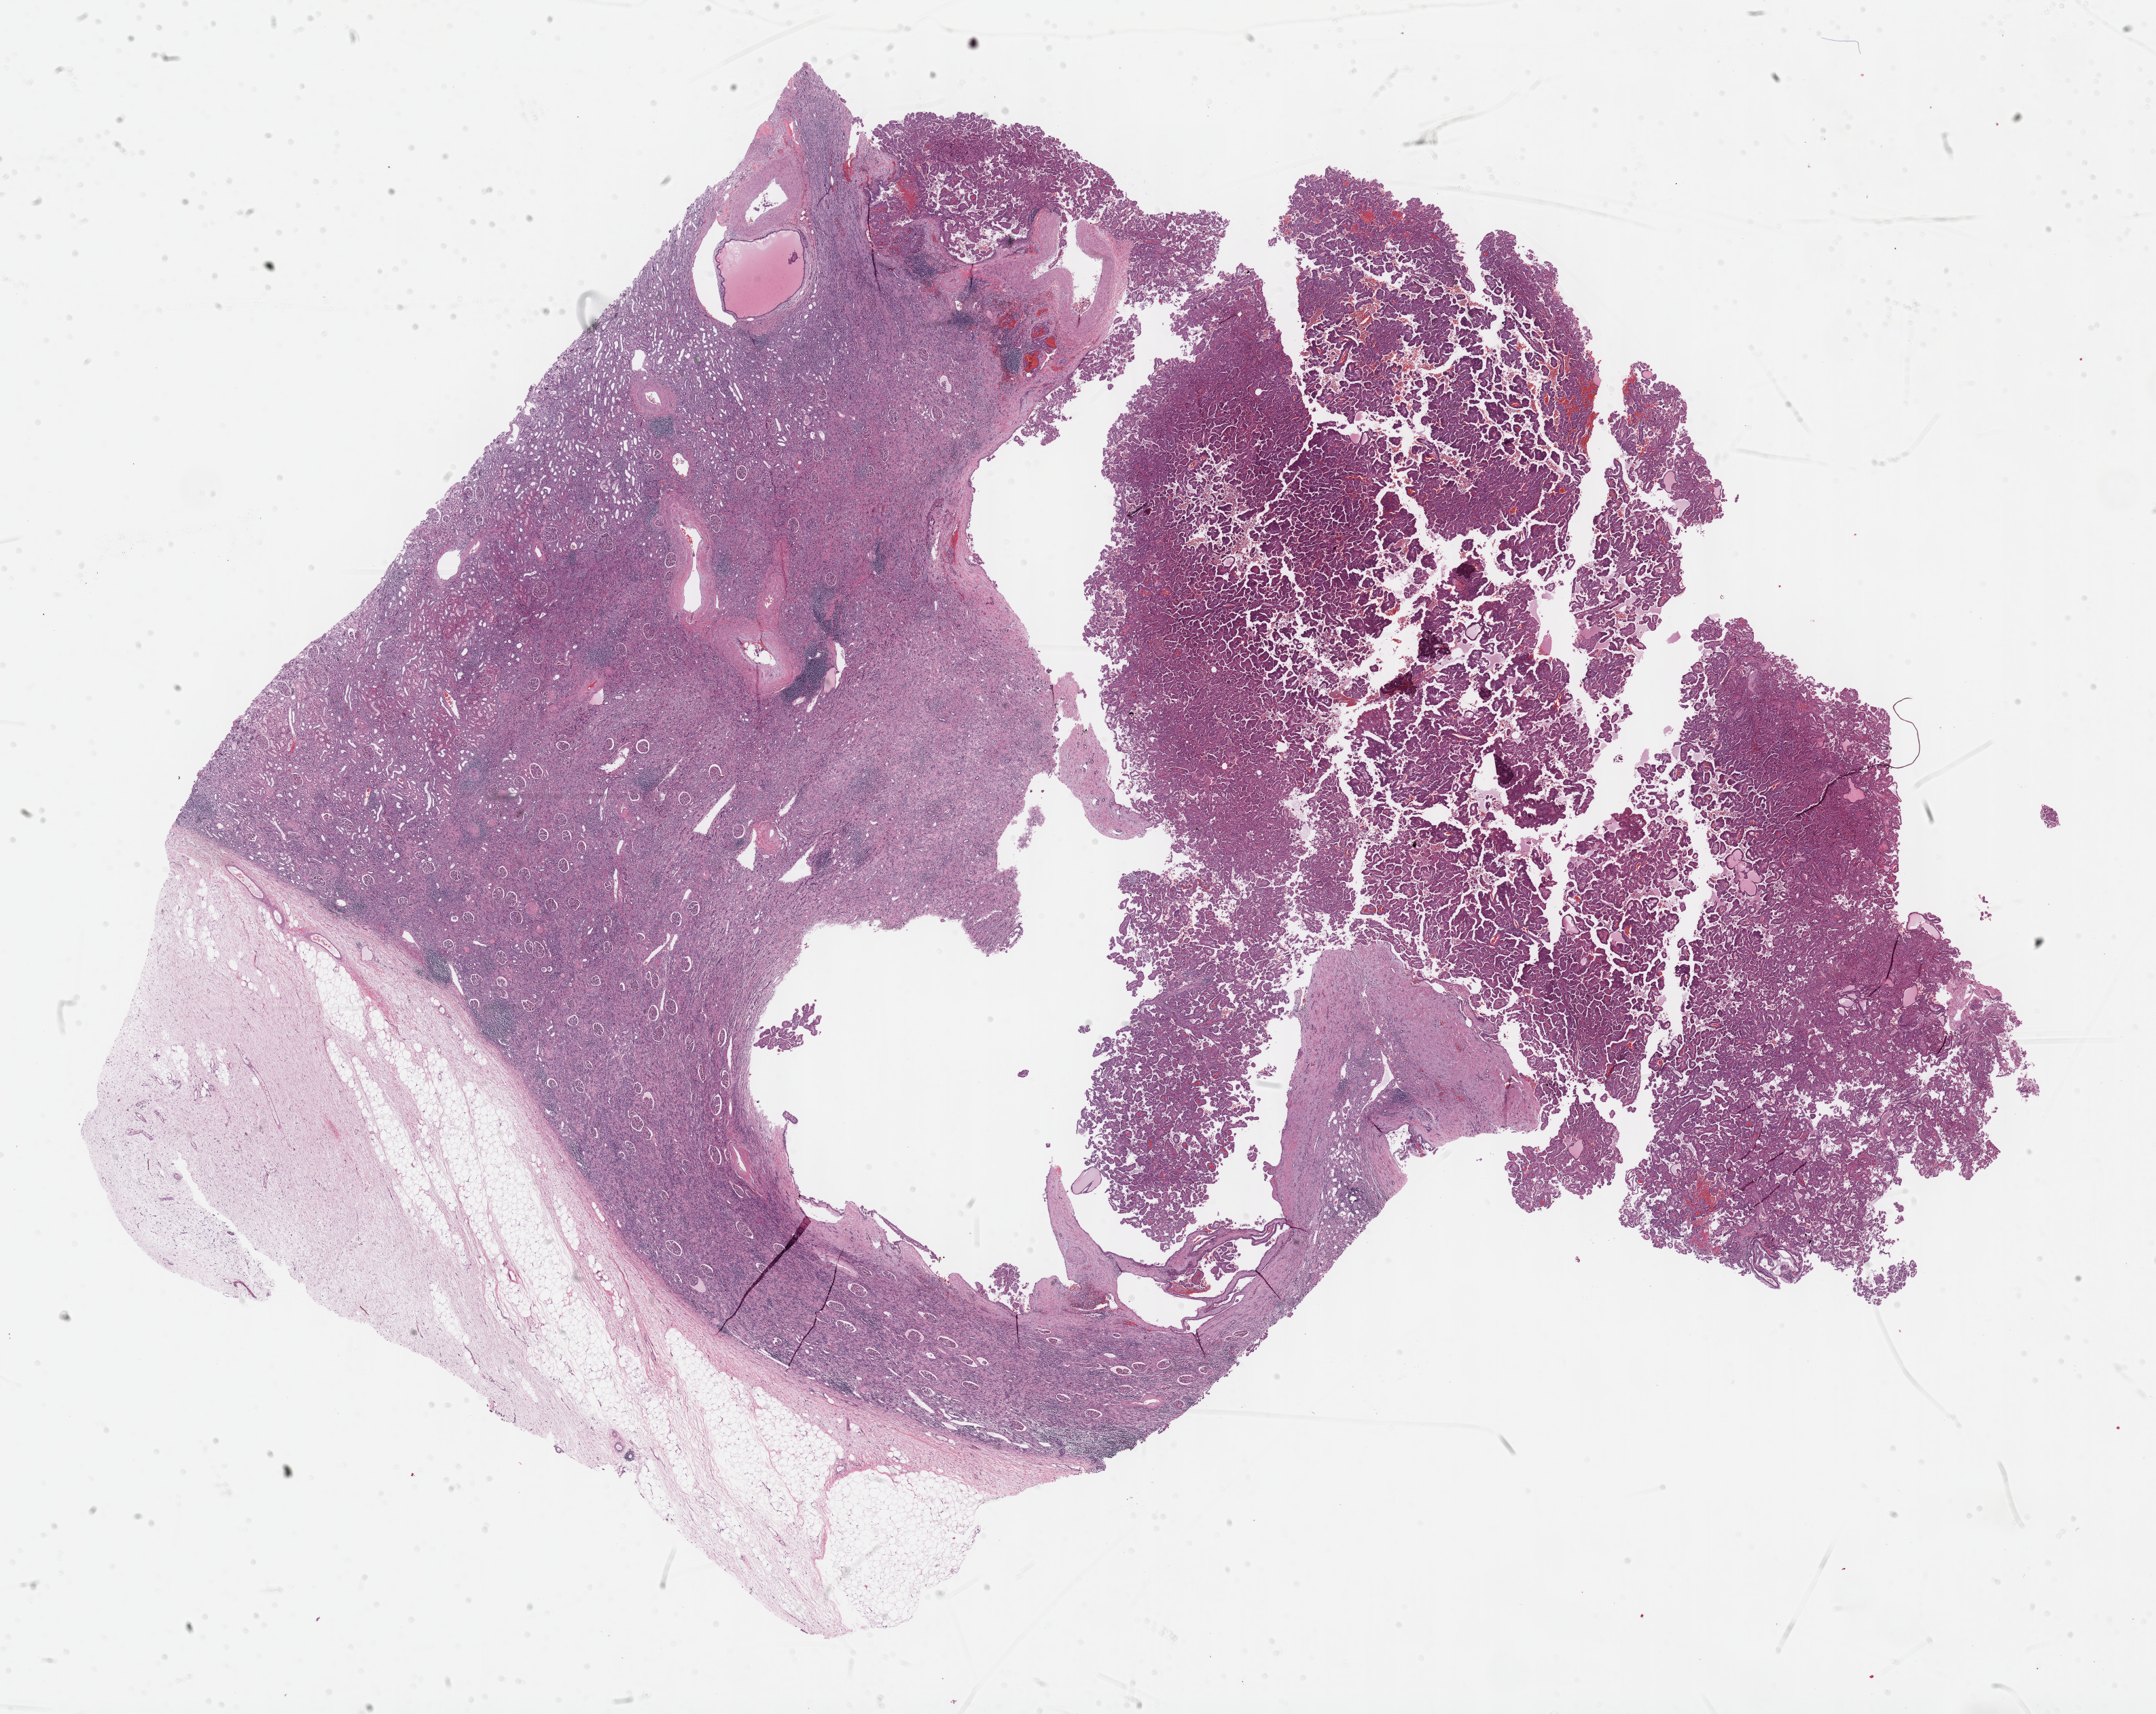
Whole-slide histology image, H&E-stained, whole scanned area (about 25.7 x 20.4 mm, acquisition: 40x scan) shown as a low-resolution overview. Formalin-fixed paraffin-embedded (FFPE) diagnostic section. Sample: primary tumour, kidney. Patient: male, age at initial diagnosis 58 years.
Histologic diagnosis: Papillary adenocarcinoma, NOS. AJCC pathologic stage: IV (7th edition). Laterality: right.